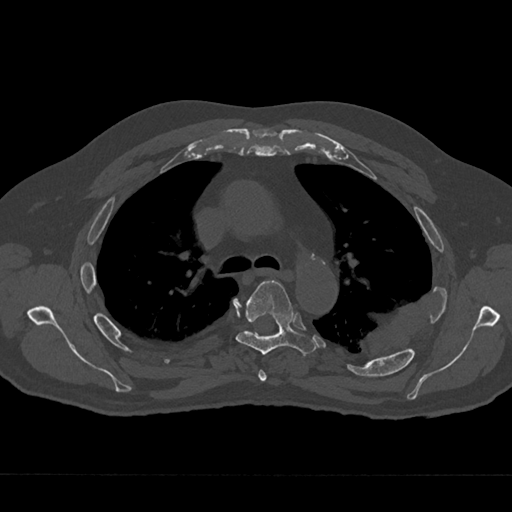
CT including the spine, one axial slice. Slice 477 of 797 in the series (ordered by position). Reconstruction kernel Br40s/3. 120 kVp. Bone window (W 1800 / L 400 HU). 512 × 512 image matrix. Male patient, age 75 years. Case-level facts recorded for this patient, not image findings: primary cancer: renal; vertebrae with lytic lesions (as recorded): T4.
Structures marked on this image (semi-automatic segmentation, software-assisted and operator-edited):
- T4 vertebra: bounding box [x1, y1, x2, y2] px = [258, 370, 267, 382]
- T5 vertebra: [235, 281, 316, 356]